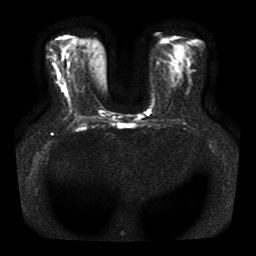
Breast MRI, one axial slice; slice 21 of 41 in the series (ordered by position); diffusion-weighted series; image 2 of 4 stored at this slice position (different b-values; order by instance number); 1.5 T; 256 × 256 image matrix. Female patient.
Structures marked on this image (expert manual segmentation):
- tumour on diffusion-weighted imaging: bounding box [x1, y1, x2, y2] px = [61, 86, 66, 92]